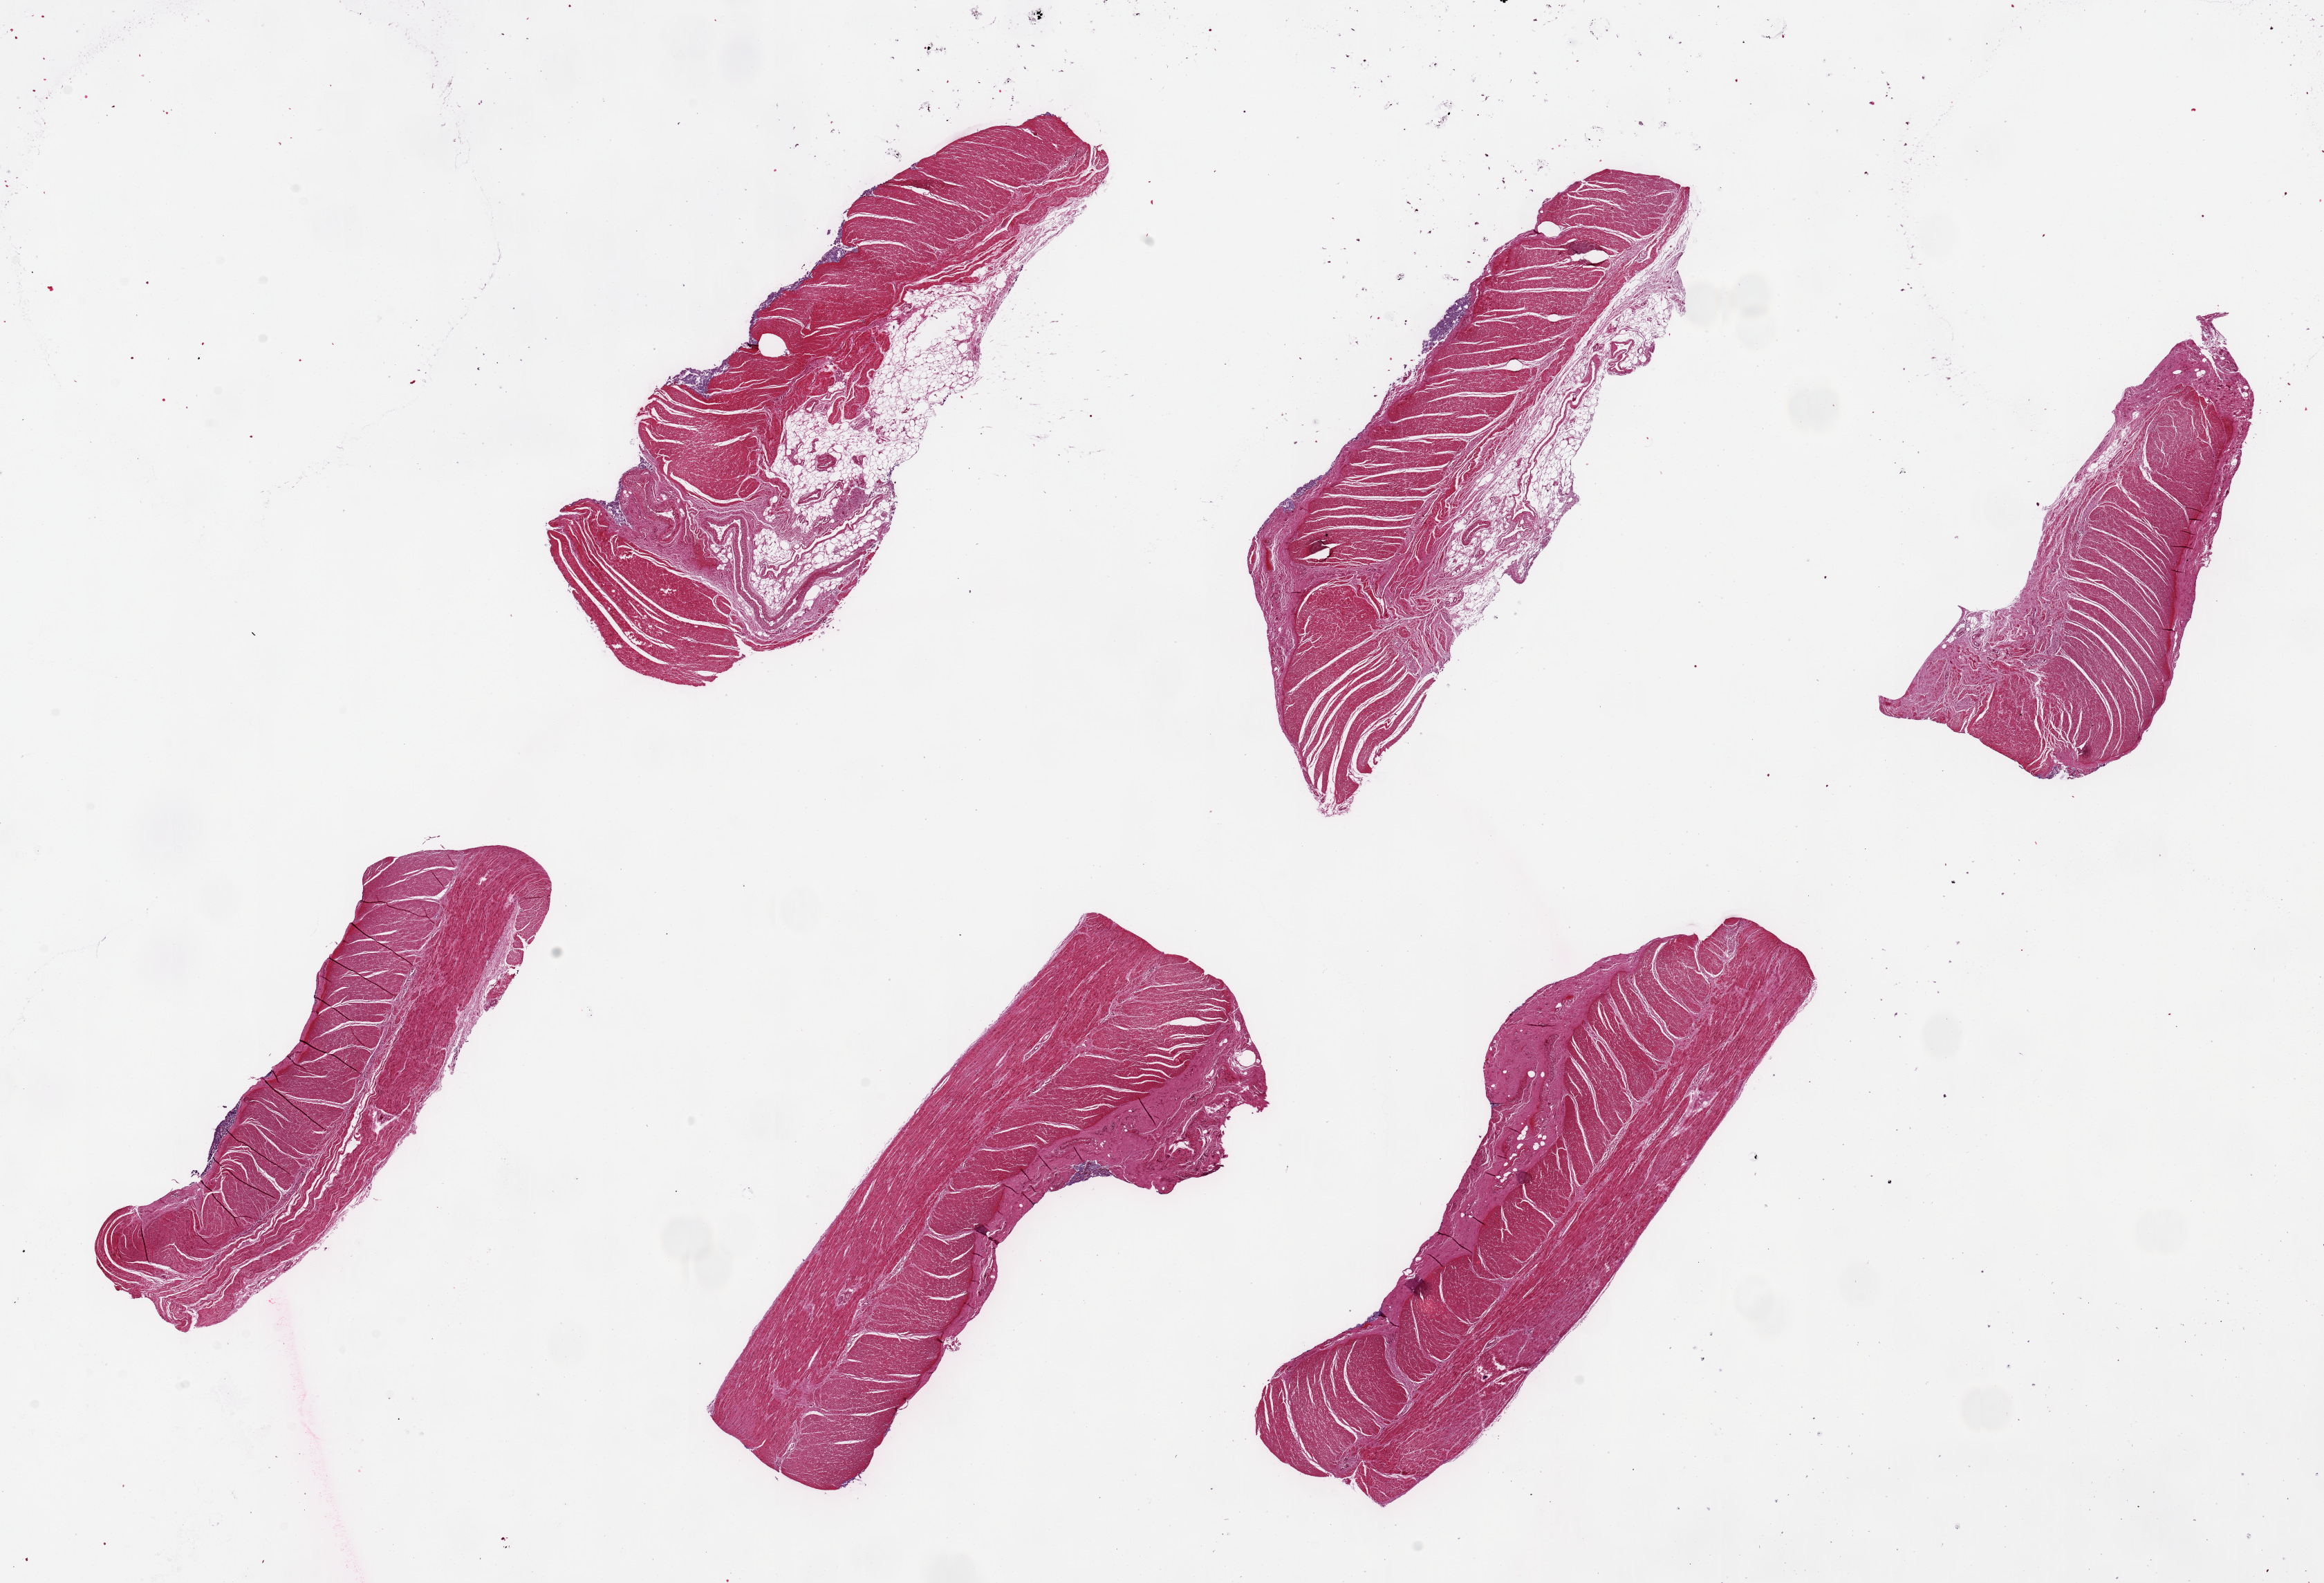
Digitized hematoxylin and eosin (H&E)-stained section, shown as a low-resolution overview of the whole scanned area (about 26.6 x 18.1 mm); PAXgene-fixed, paraffin-embedded tissue; target tissue: sigmoid colon; tissue donor sample. Donor: male.
Review note (as recorded): 6 pieces, up to 8x3mm; mainly muscularis; ~10-15% fat.